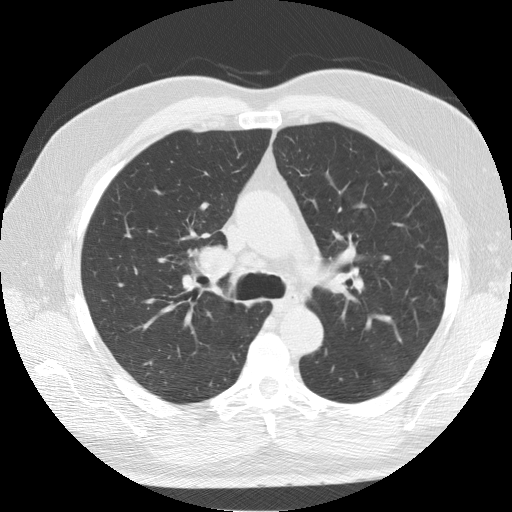
Low-dose screening chest CT, one axial slice. Slice 95 of 139 in the series (ordered by position). Lung window (W 1500 / L -600 HU). 2.5 mm slice thickness. 512 × 512 image matrix.
Annotated regions visible in this slice (manually delineated by an expert):
- lesion 1 (tumor, upper lobe of right lung): box from (x=199, y=247) to (x=233, y=280) px